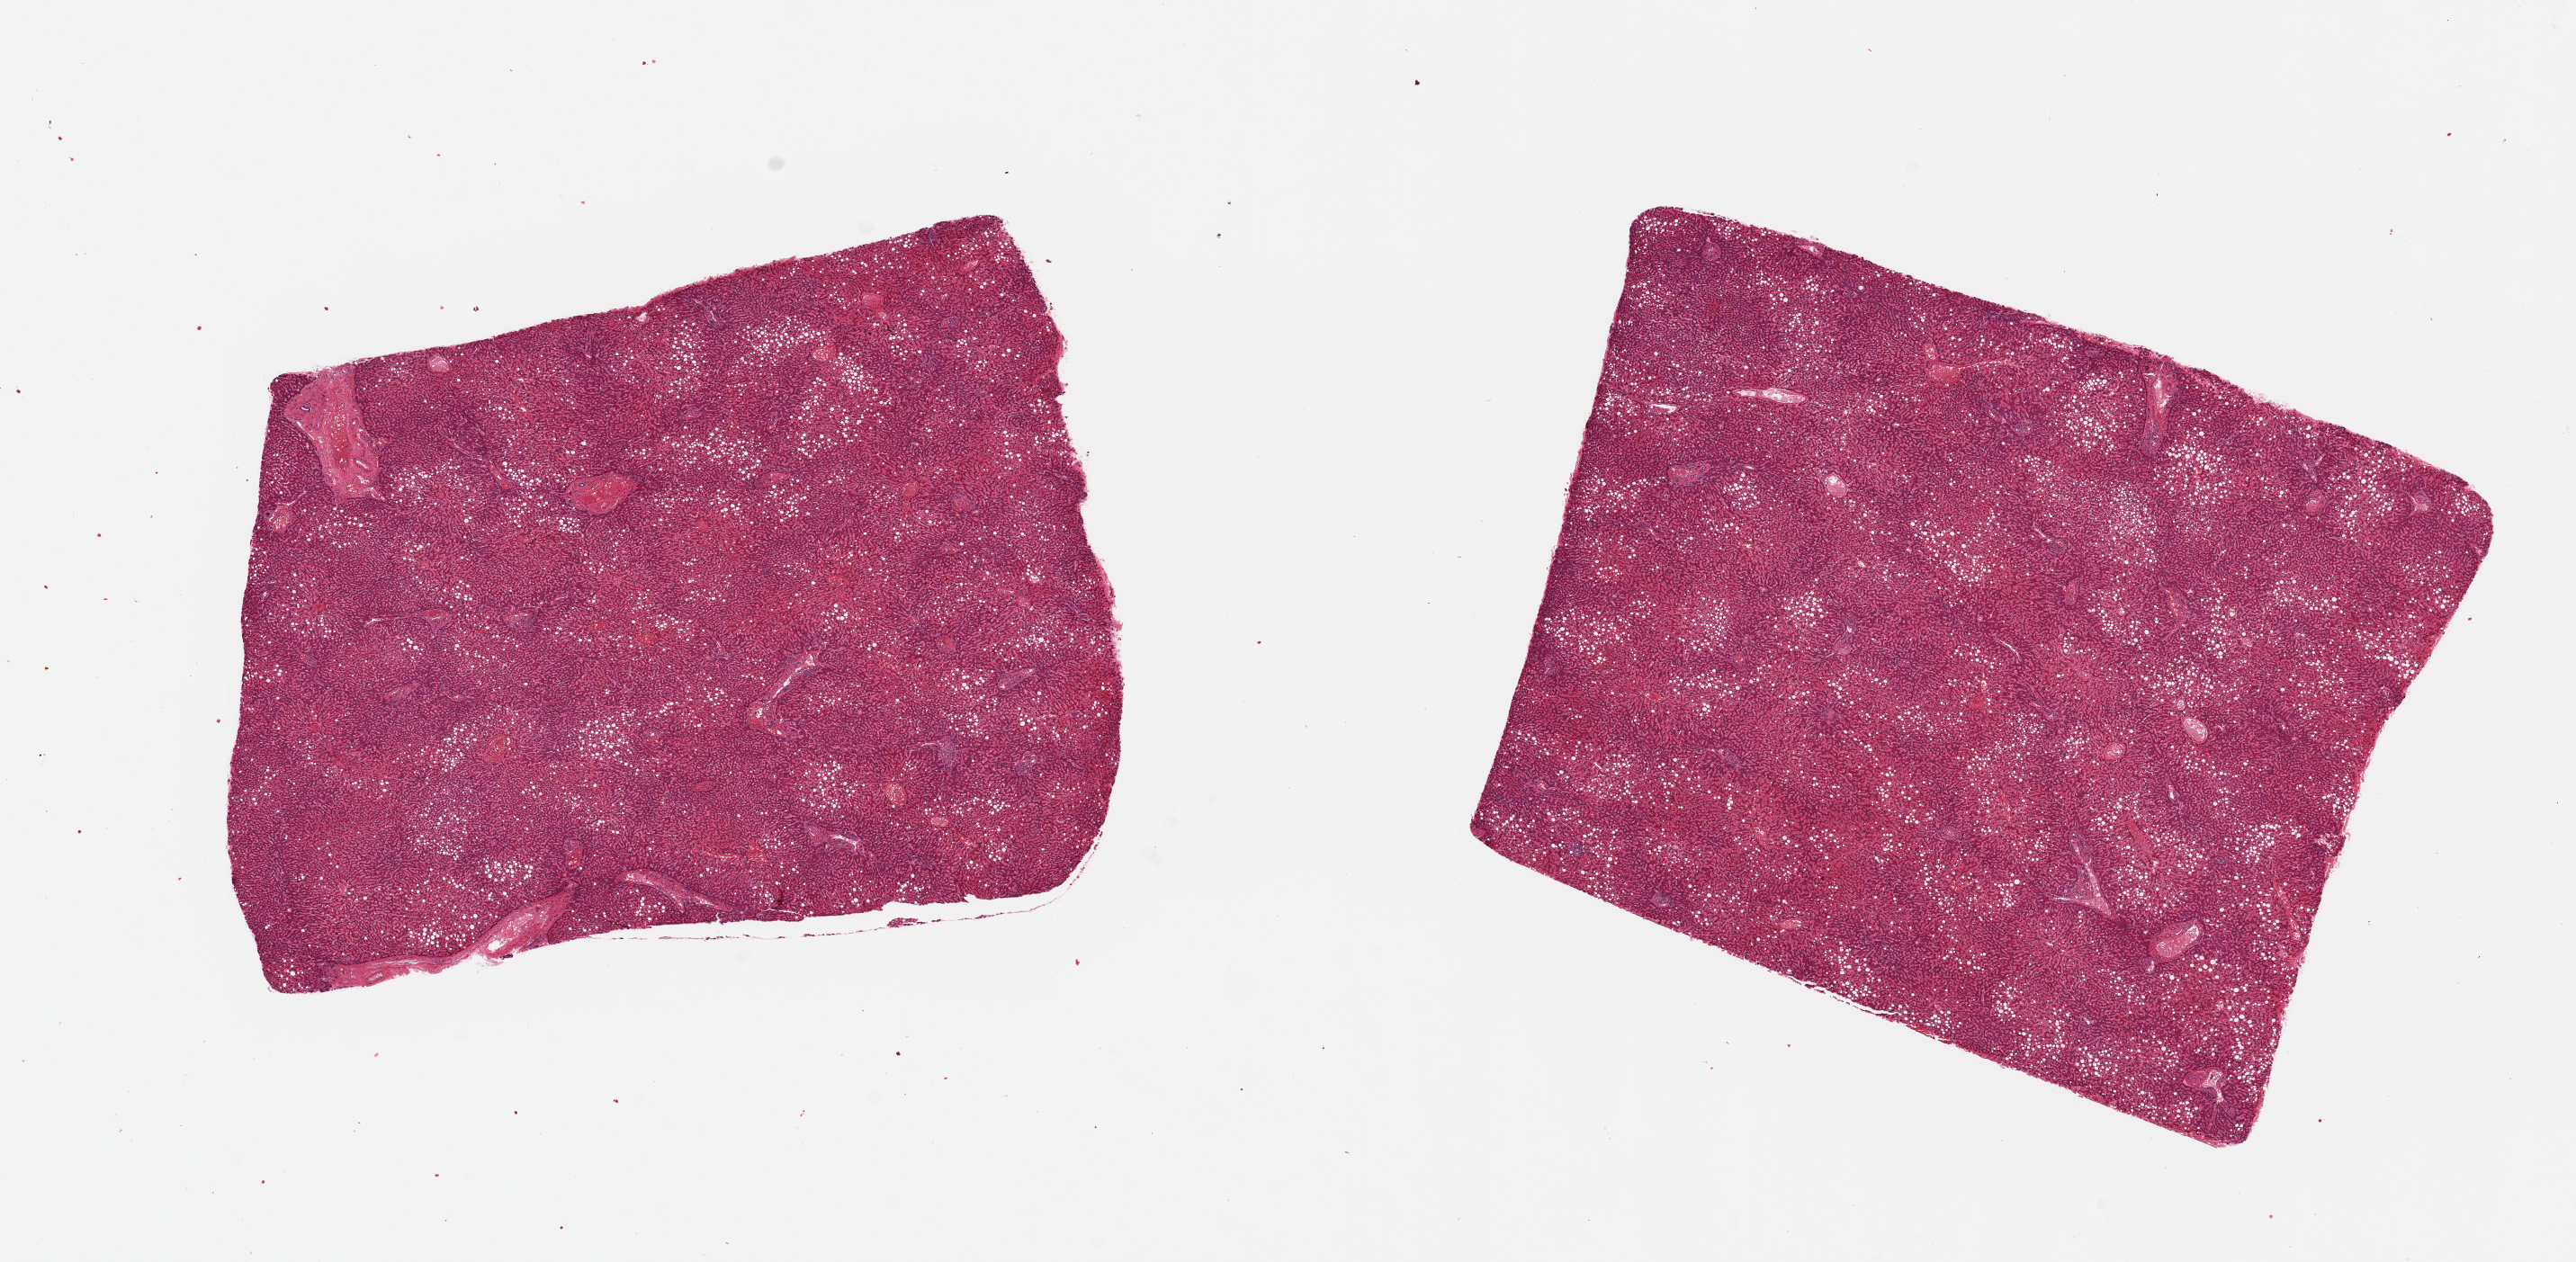
Whole-slide image, H&E stain, brightfield — whole scanned area (about 22.6 x 11.1 mm, slide scanned at 20x) shown as a low-resolution overview. PAXgene-fixed, paraffin-embedded tissue. Section of liver (target tissue). Tissue donor sample. Donor sex: male.
Reviewer comment on this tissue sample: 2 pieces ~7x6mm. Diffuse macrovesicular steatosis involves ~30% of parenchyma.